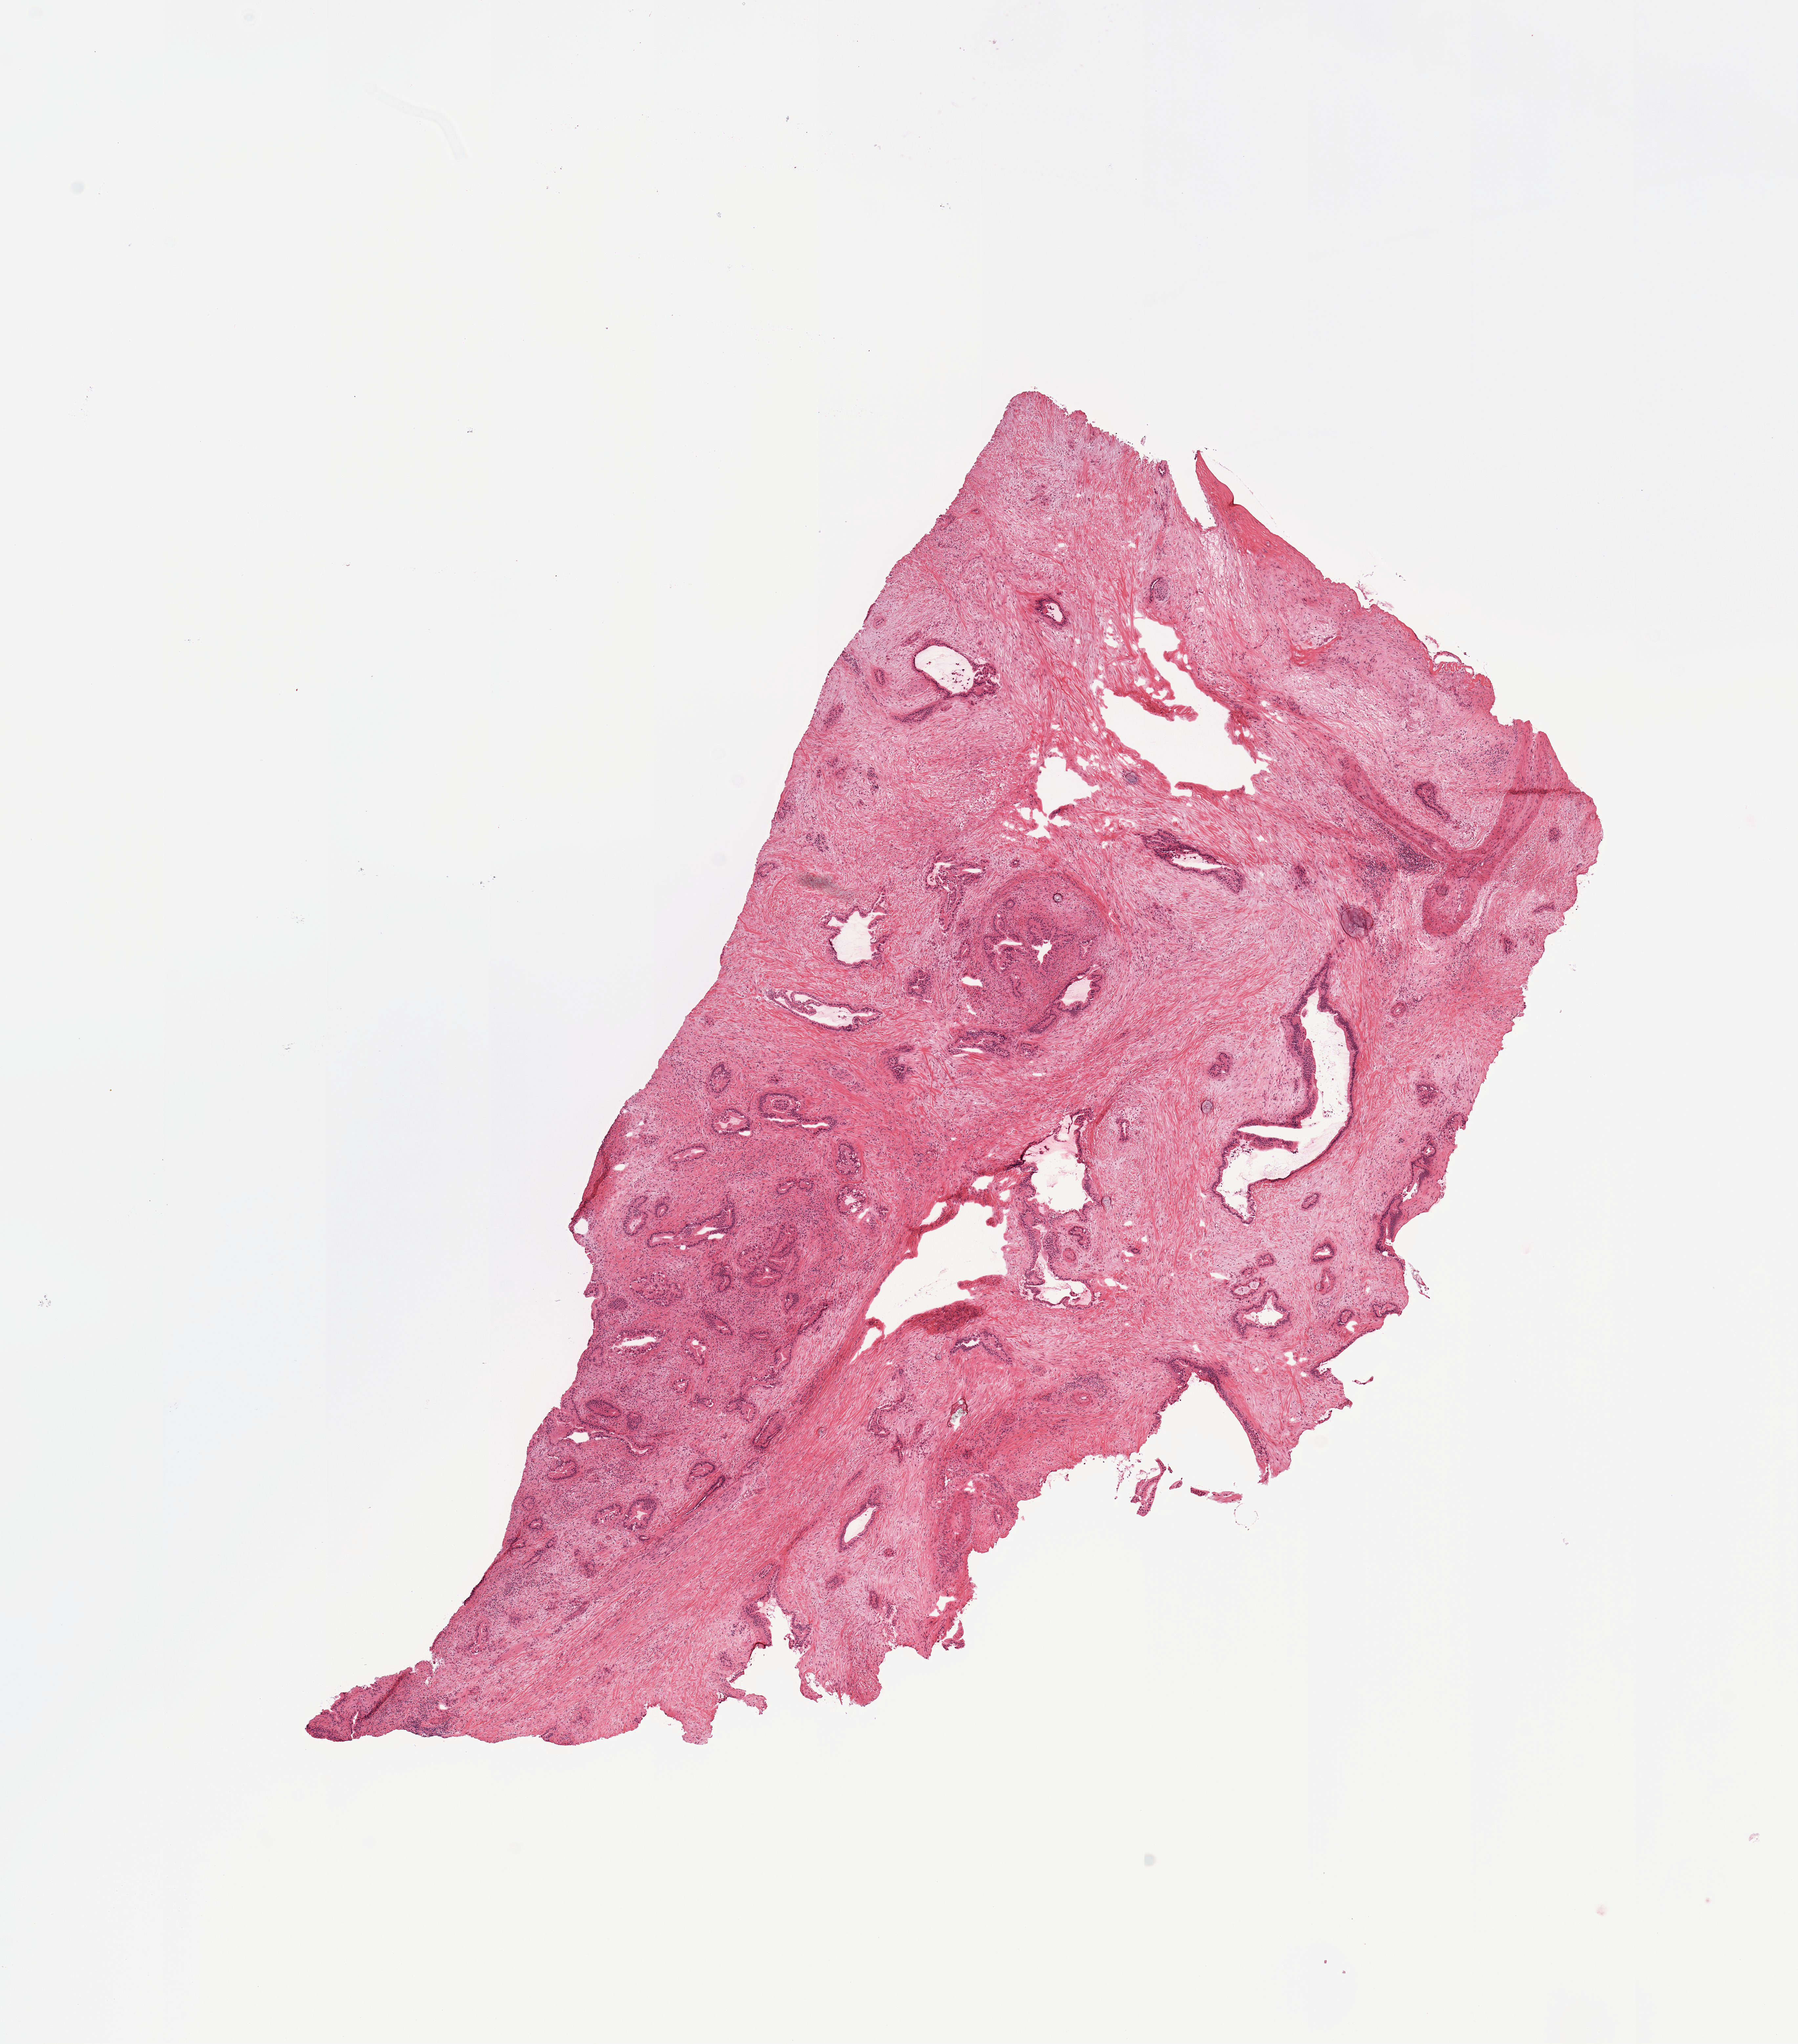
Whole-slide histology image, H&E-stained — whole scanned area (about 10.8 x 12.3 mm) shown as a low-resolution overview, tumour tissue sample, sampled site: pancreas. Patient: male, age 62 years. Histologic grade: G1 (well differentiated). Slide review estimates, as recorded: tumour nuclei 25%, necrosis 0%.
AJCC pathologic stage: IIB. Diagnosis: Infiltrating duct carcinoma, NOS.